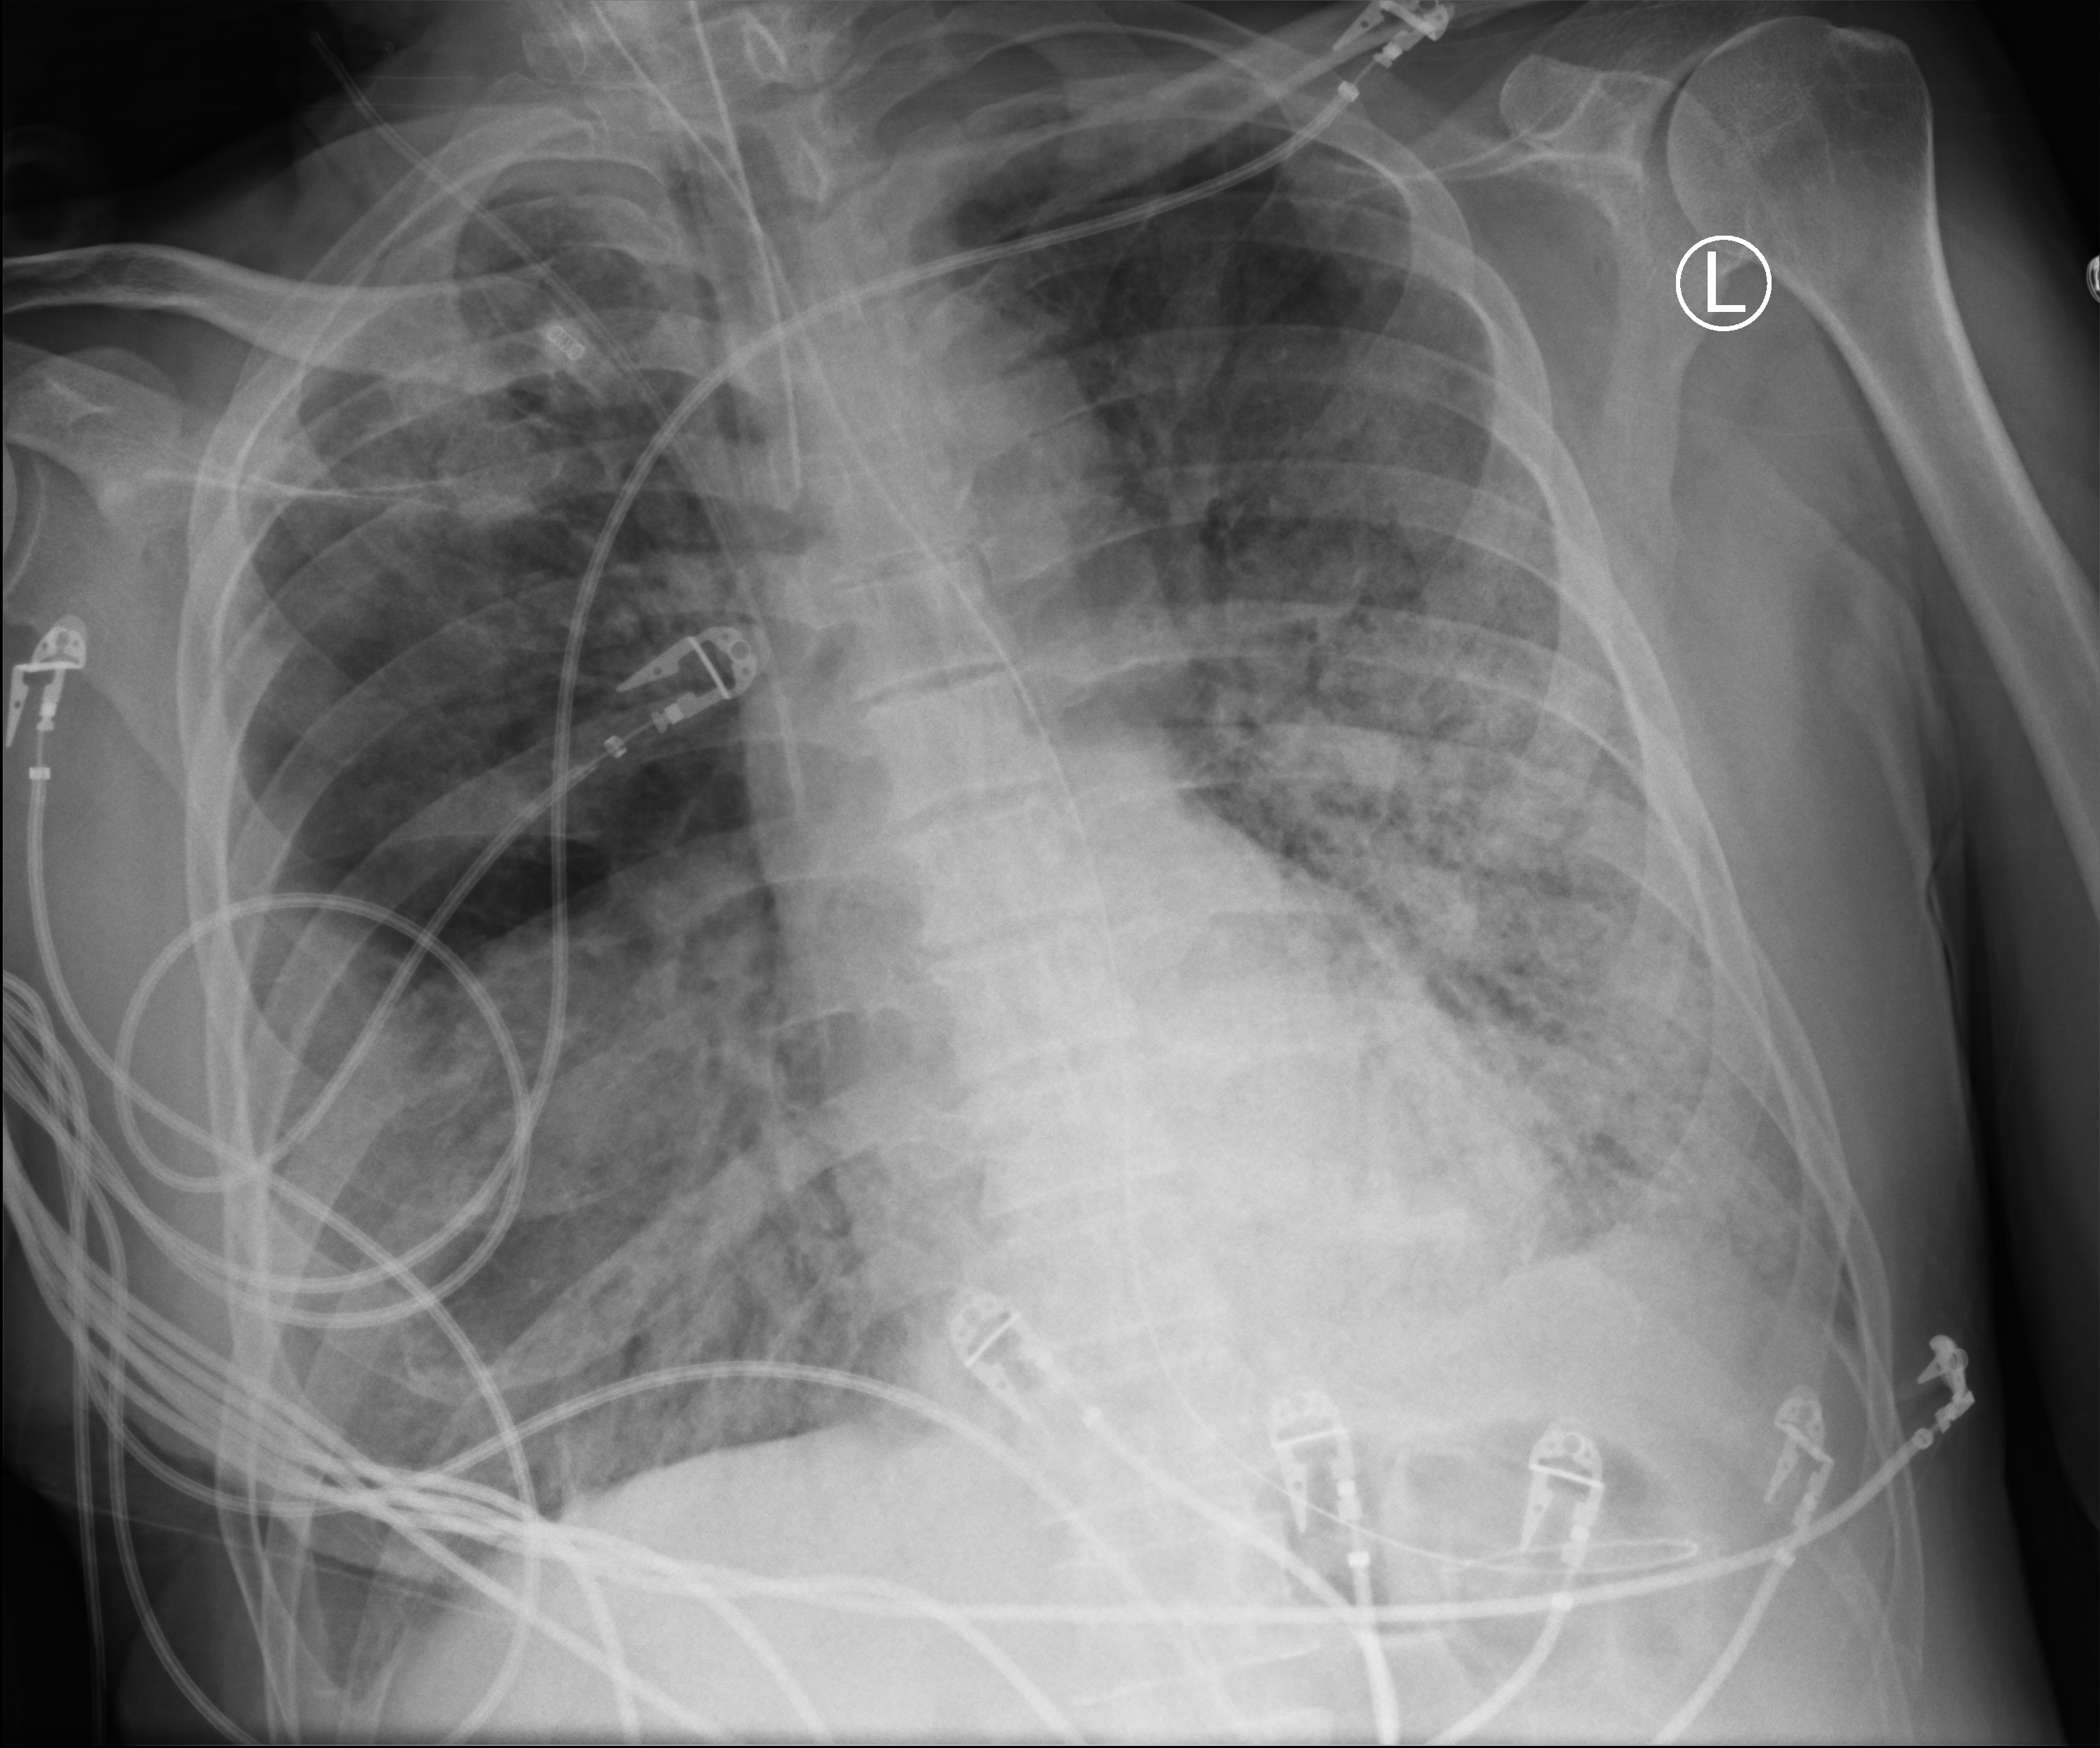
Chest X-ray (portable). Patient hospitalised with COVID-19; male, aged 60–74 years.
Admission-level facts for this patient (not findings on this image; timing relative to this image not recorded): mechanically ventilated during this hospital stay: yes; chronic kidney disease (admission record): no; admitted to intensive care during this hospital stay: yes.